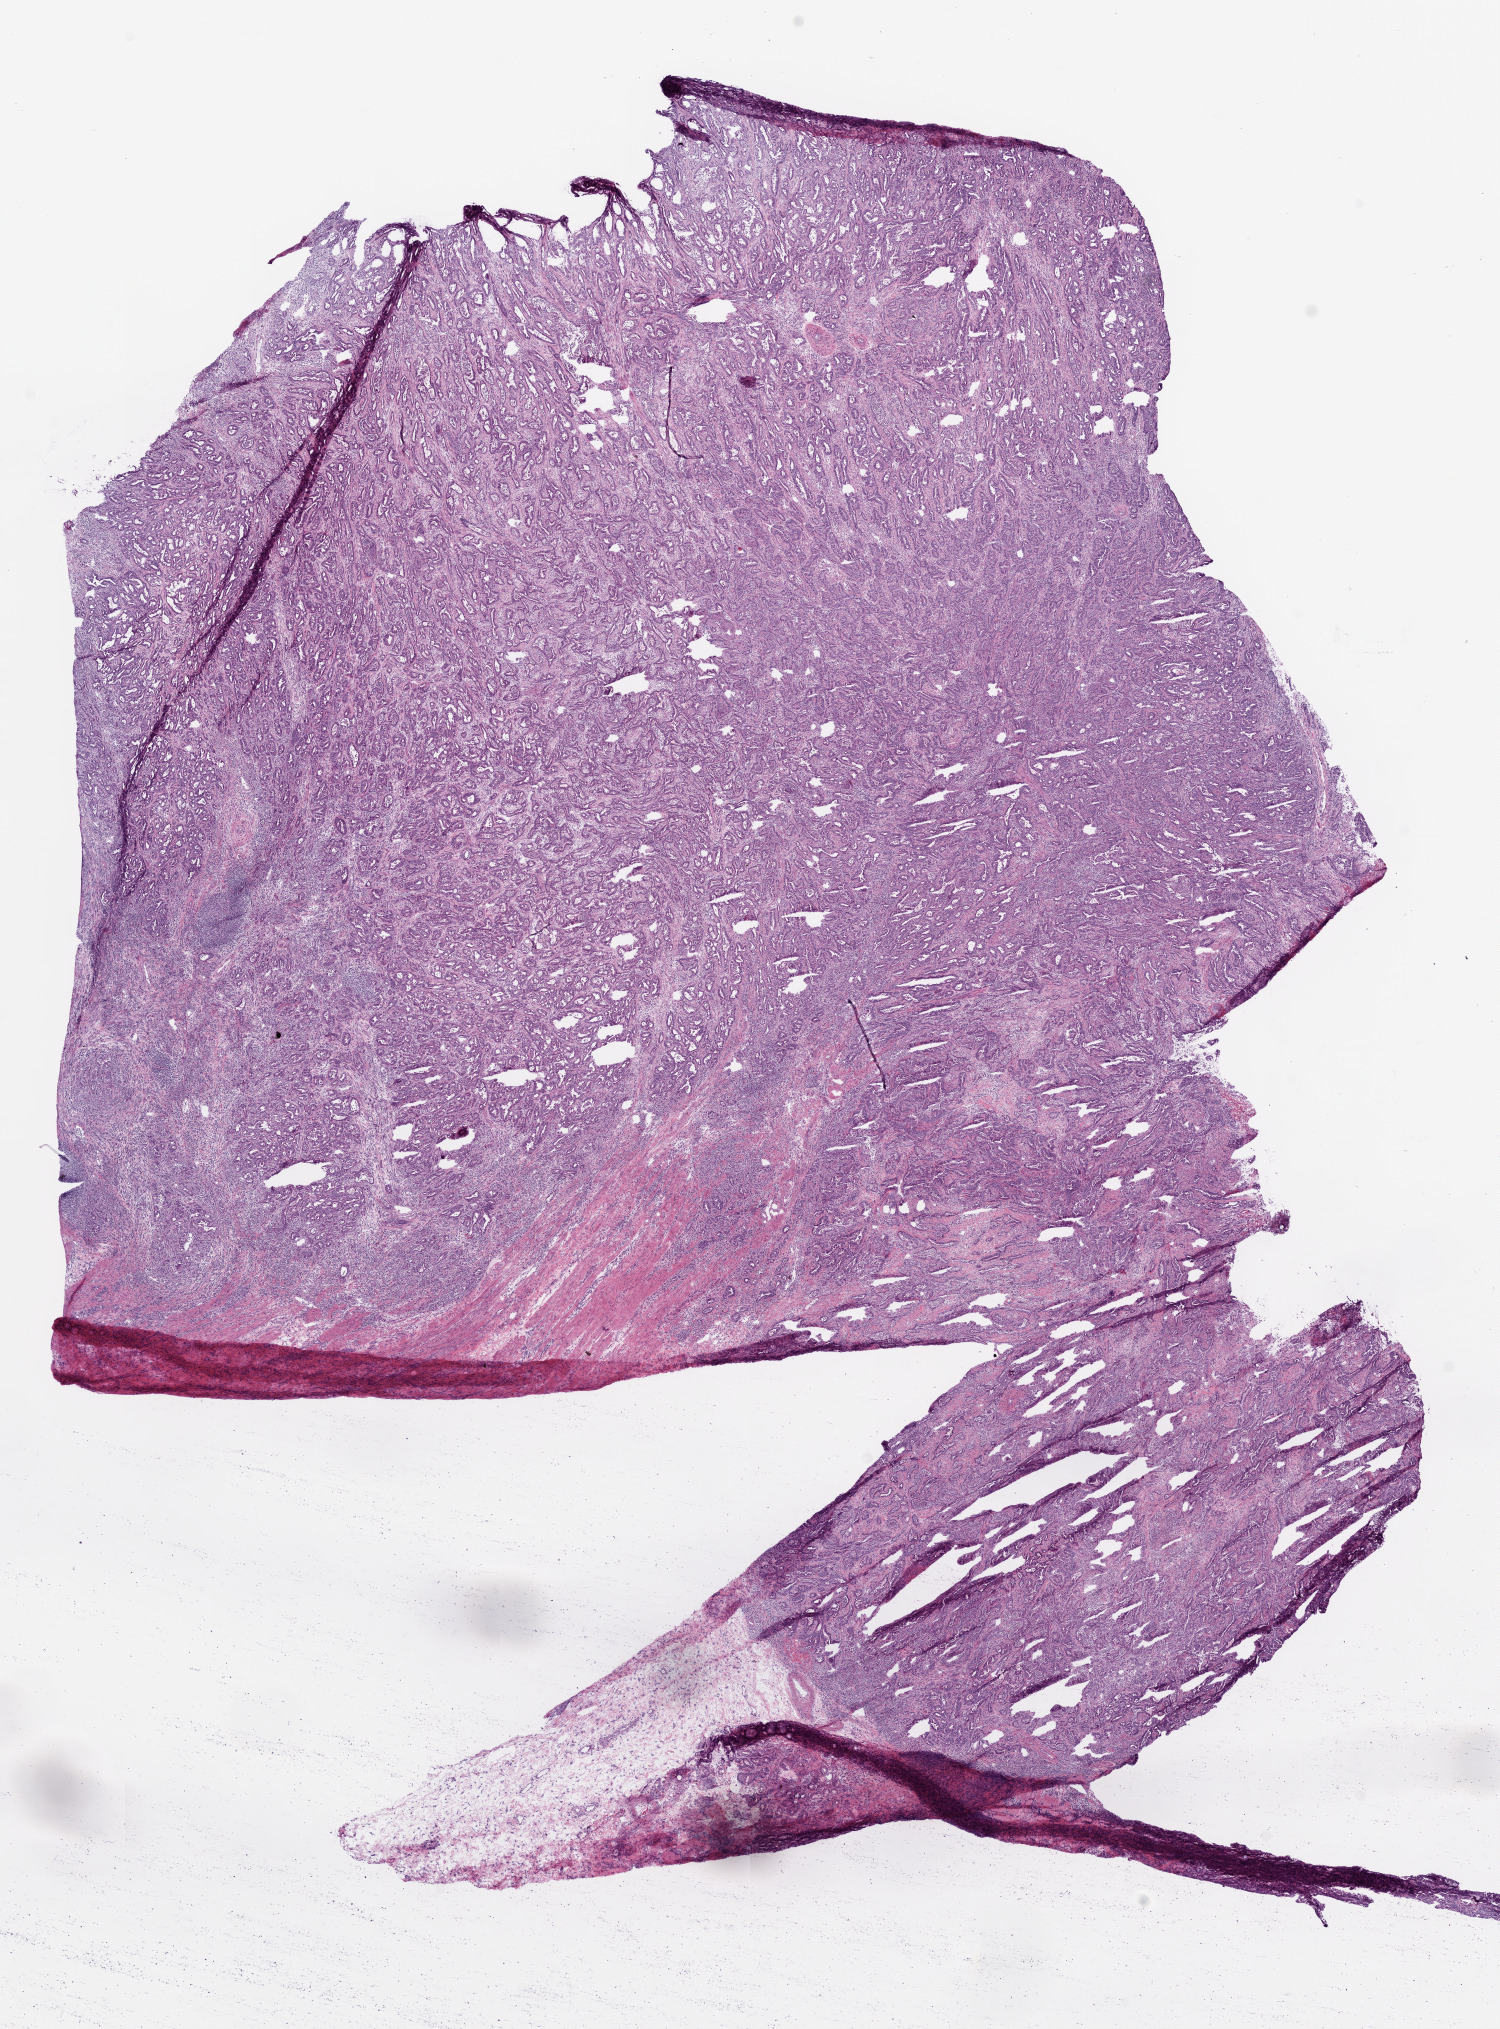
Digitized H&E-stained tissue section (whole slide) — low-resolution overview of the scanned area, about 12.0 x 16.3 mm (from a 20x scan), frozen section, sample: primary tumour, stomach. Female, age 74 years at initial diagnosis. Histologic grade: G2 (moderately differentiated). Composition of this section per pathologist review: tumour cells 80%, tumour nuclei 75%, normal cells 10%, stromal cells 5%, necrosis 5%.
Histologic diagnosis: Adenocarcinoma, NOS (gastric antrum).